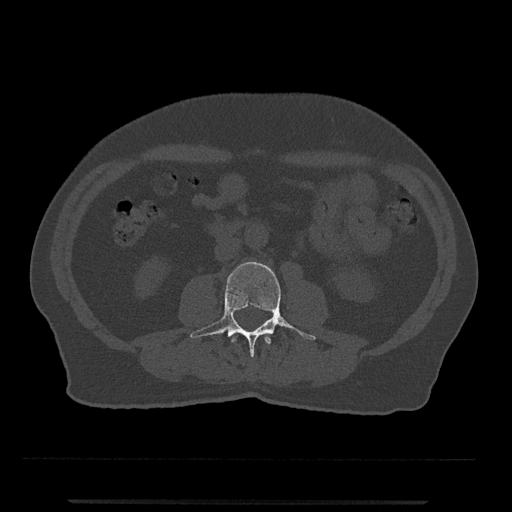
CT including the spine, one axial slice. Reconstruction kernel Br40s/3. 120 kVp. Bone window (W 1800 / L 400 HU). 0.5 mm slice thickness. 512 × 512 image matrix, field of view 419 × 419 mm. Patient: male, 63 years. From the clinical record (not read from this slice): primary cancer: prostate.
Outlined on this slice (semi-automatically segmented with operator editing):
- L2 vertebra: bounding box (x1, y1, x2, y2) in pixels: (231, 334, 271, 345)
- L3 vertebra: (190, 262, 316, 357)